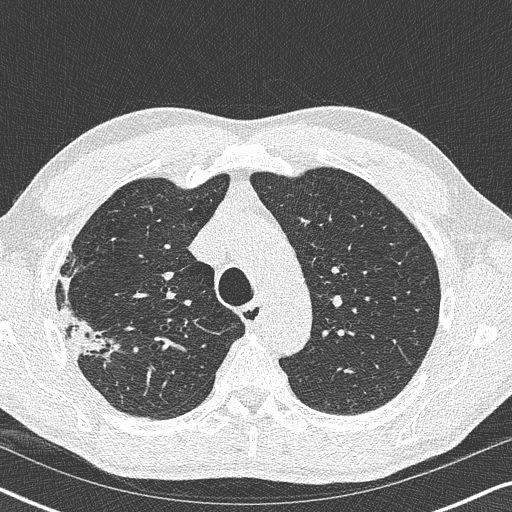
Low-dose screening chest CT, one axial slice. Position 273 of 356 along the scan axis. Reconstruction kernel B50f. Lung window (W 1500 / L -600 HU). 1 mm slice thickness. 512 × 512 image matrix, field of view 330 × 330 mm.
Outlined on this slice (manually delineated by an expert):
- lesion 1 (tumor, upper lobe of right lung): box from (x=57, y=305) to (x=121, y=359) px